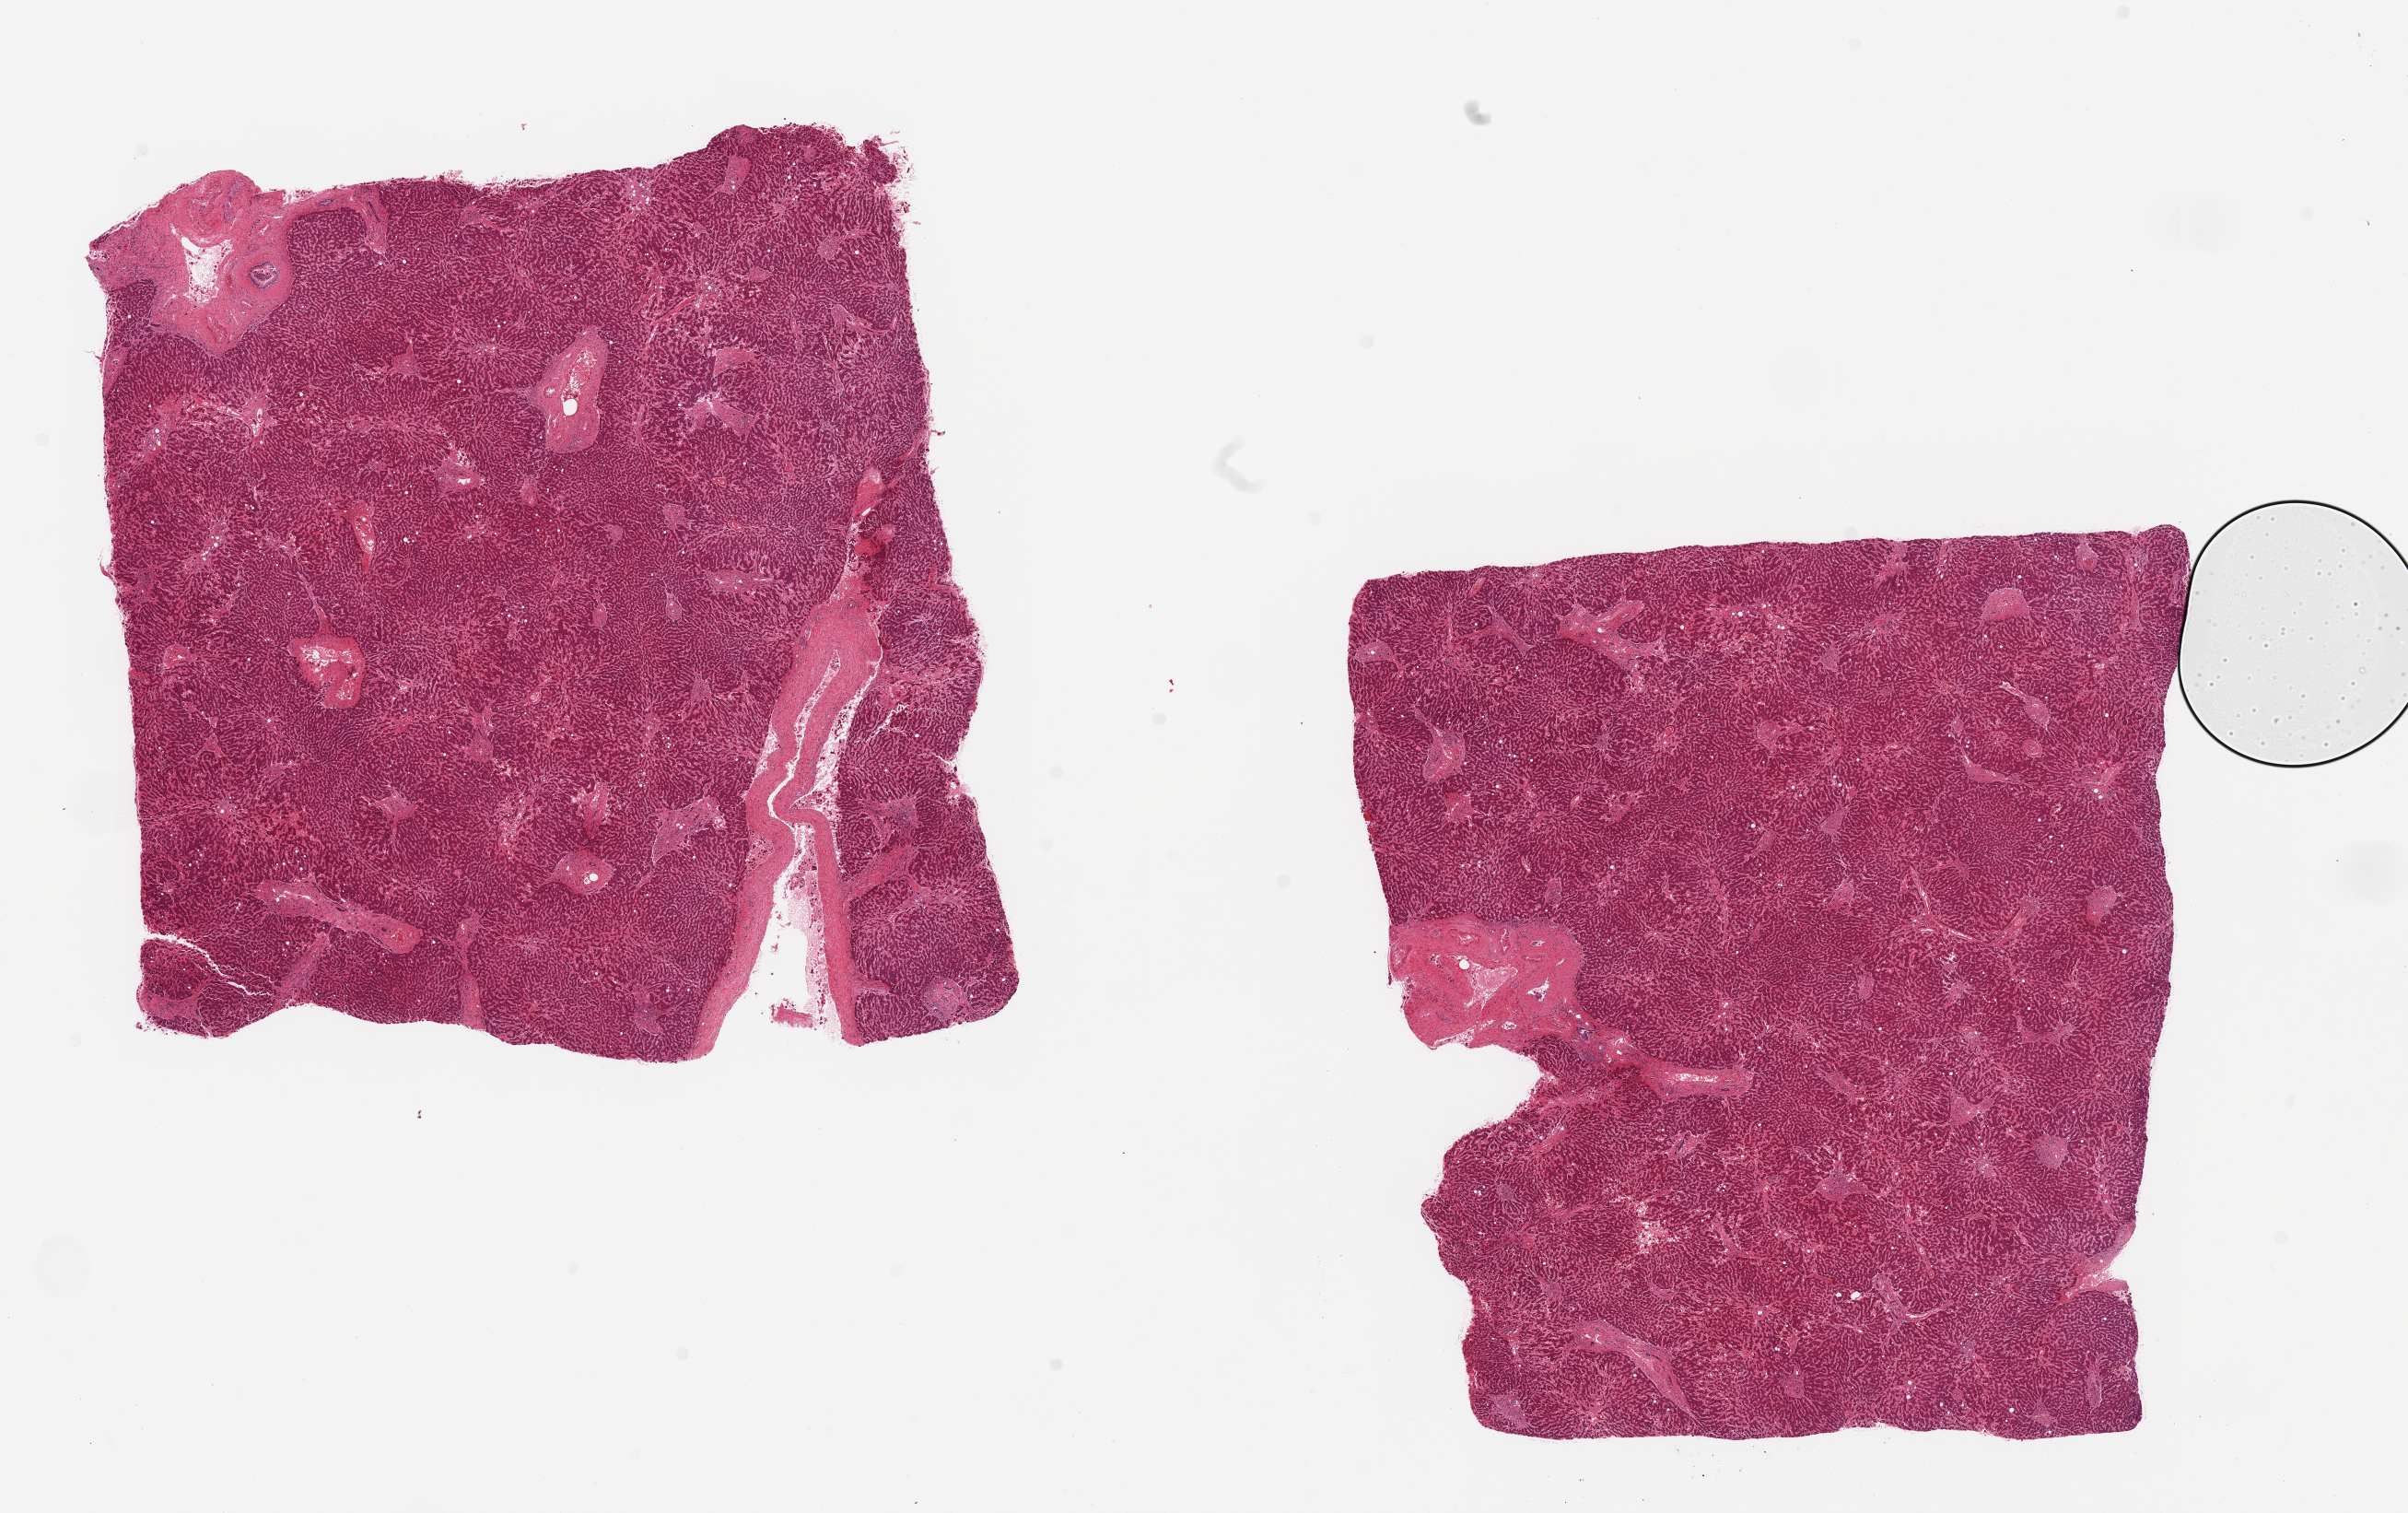
Hematoxylin and eosin (H&E) whole-slide image, brightfield — low-resolution overview of the scanned area, about 20.7 x 13.0 mm (acquisition: 20x scan), PAXgene-fixed, paraffin-embedded tissue, target tissue: liver, donor tissue sample. Male donor.
Reviewer comment on this tissue sample: 2 pieces mild macrovesicular steatosis (10-20%).